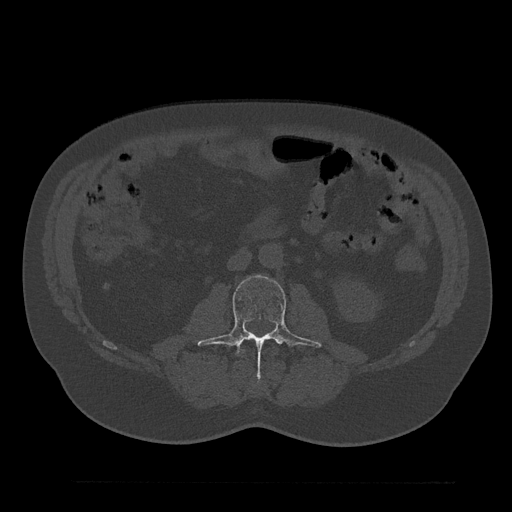
CT including the spine, one axial slice. Slice 40 of 797 in the series (ordered by position). 120 kVp. Bone window (W 1800 / L 400 HU). 0.5 mm slice thickness. 512 × 512 image matrix, field of view 430 × 430 mm. Patient: male, 61 years. From the clinical record (not read from this slice): primary cancer: prostate.
Outlined on this slice (semi-automatic segmentation, software-assisted and operator-edited):
- L3 vertebra: box from (x=197, y=275) to (x=322, y=366) px